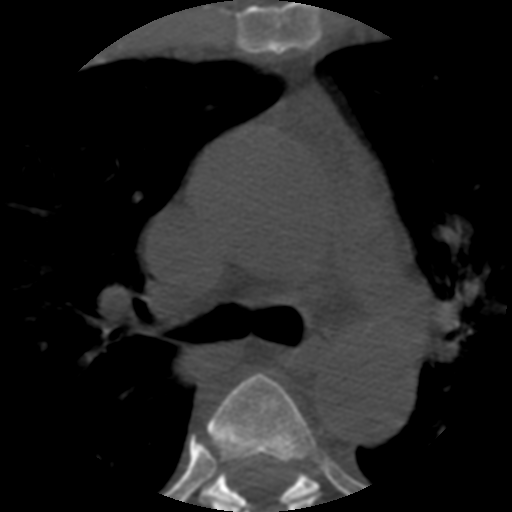
CT including the spine, one axial slice; position 386 of 508 along the scan axis; reconstruction kernel STANDARD; bone window (W 1800 / L 400 HU); 1.25 mm slice thickness; 512 × 512 image matrix, field of view 160 × 160 mm. Patient age 57 years. From the clinical record (not read from this slice): primary cancer: prostate.
Annotated regions visible in this slice (semi-automatic segmentation, software-assisted and operator-edited):
- T4 vertebra: box from (x=200, y=373) to (x=318, y=512) px
- T5 vertebra: (x=206, y=471)–(x=318, y=512)